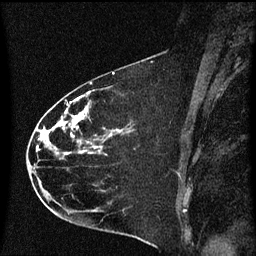
Breast MRI (dynamic contrast-enhanced), one sagittal slice; slice 36 of 60 in the series (ordered by position); dynamic contrast-enhanced series, image 2 of 3 at this slice position (ordered by acquisition); 1.5 T; TE 4.2 ms, TR 8.4 ms; 2 mm slice thickness; 256 × 256 image matrix, field of view 200 × 200 mm. Patient: female, 35 years. From the clinical record (not read from this slice): setting: breast cancer imaged before/during neoadjuvant chemotherapy; receptor status: HER2-positive.
Structures marked on this image (semi-automatic segmentation, software-assisted and operator-edited):
- analysis volume of interest (the breast-tissue region the enhancement analysis was run in; not a lesion): bounding box [x1, y1, x2, y2] px = [28, 68, 174, 173]
- tumour enhancement mask (voxels above the 70 % enhancement threshold inside the analysis volume of interest): [41, 92, 132, 155]